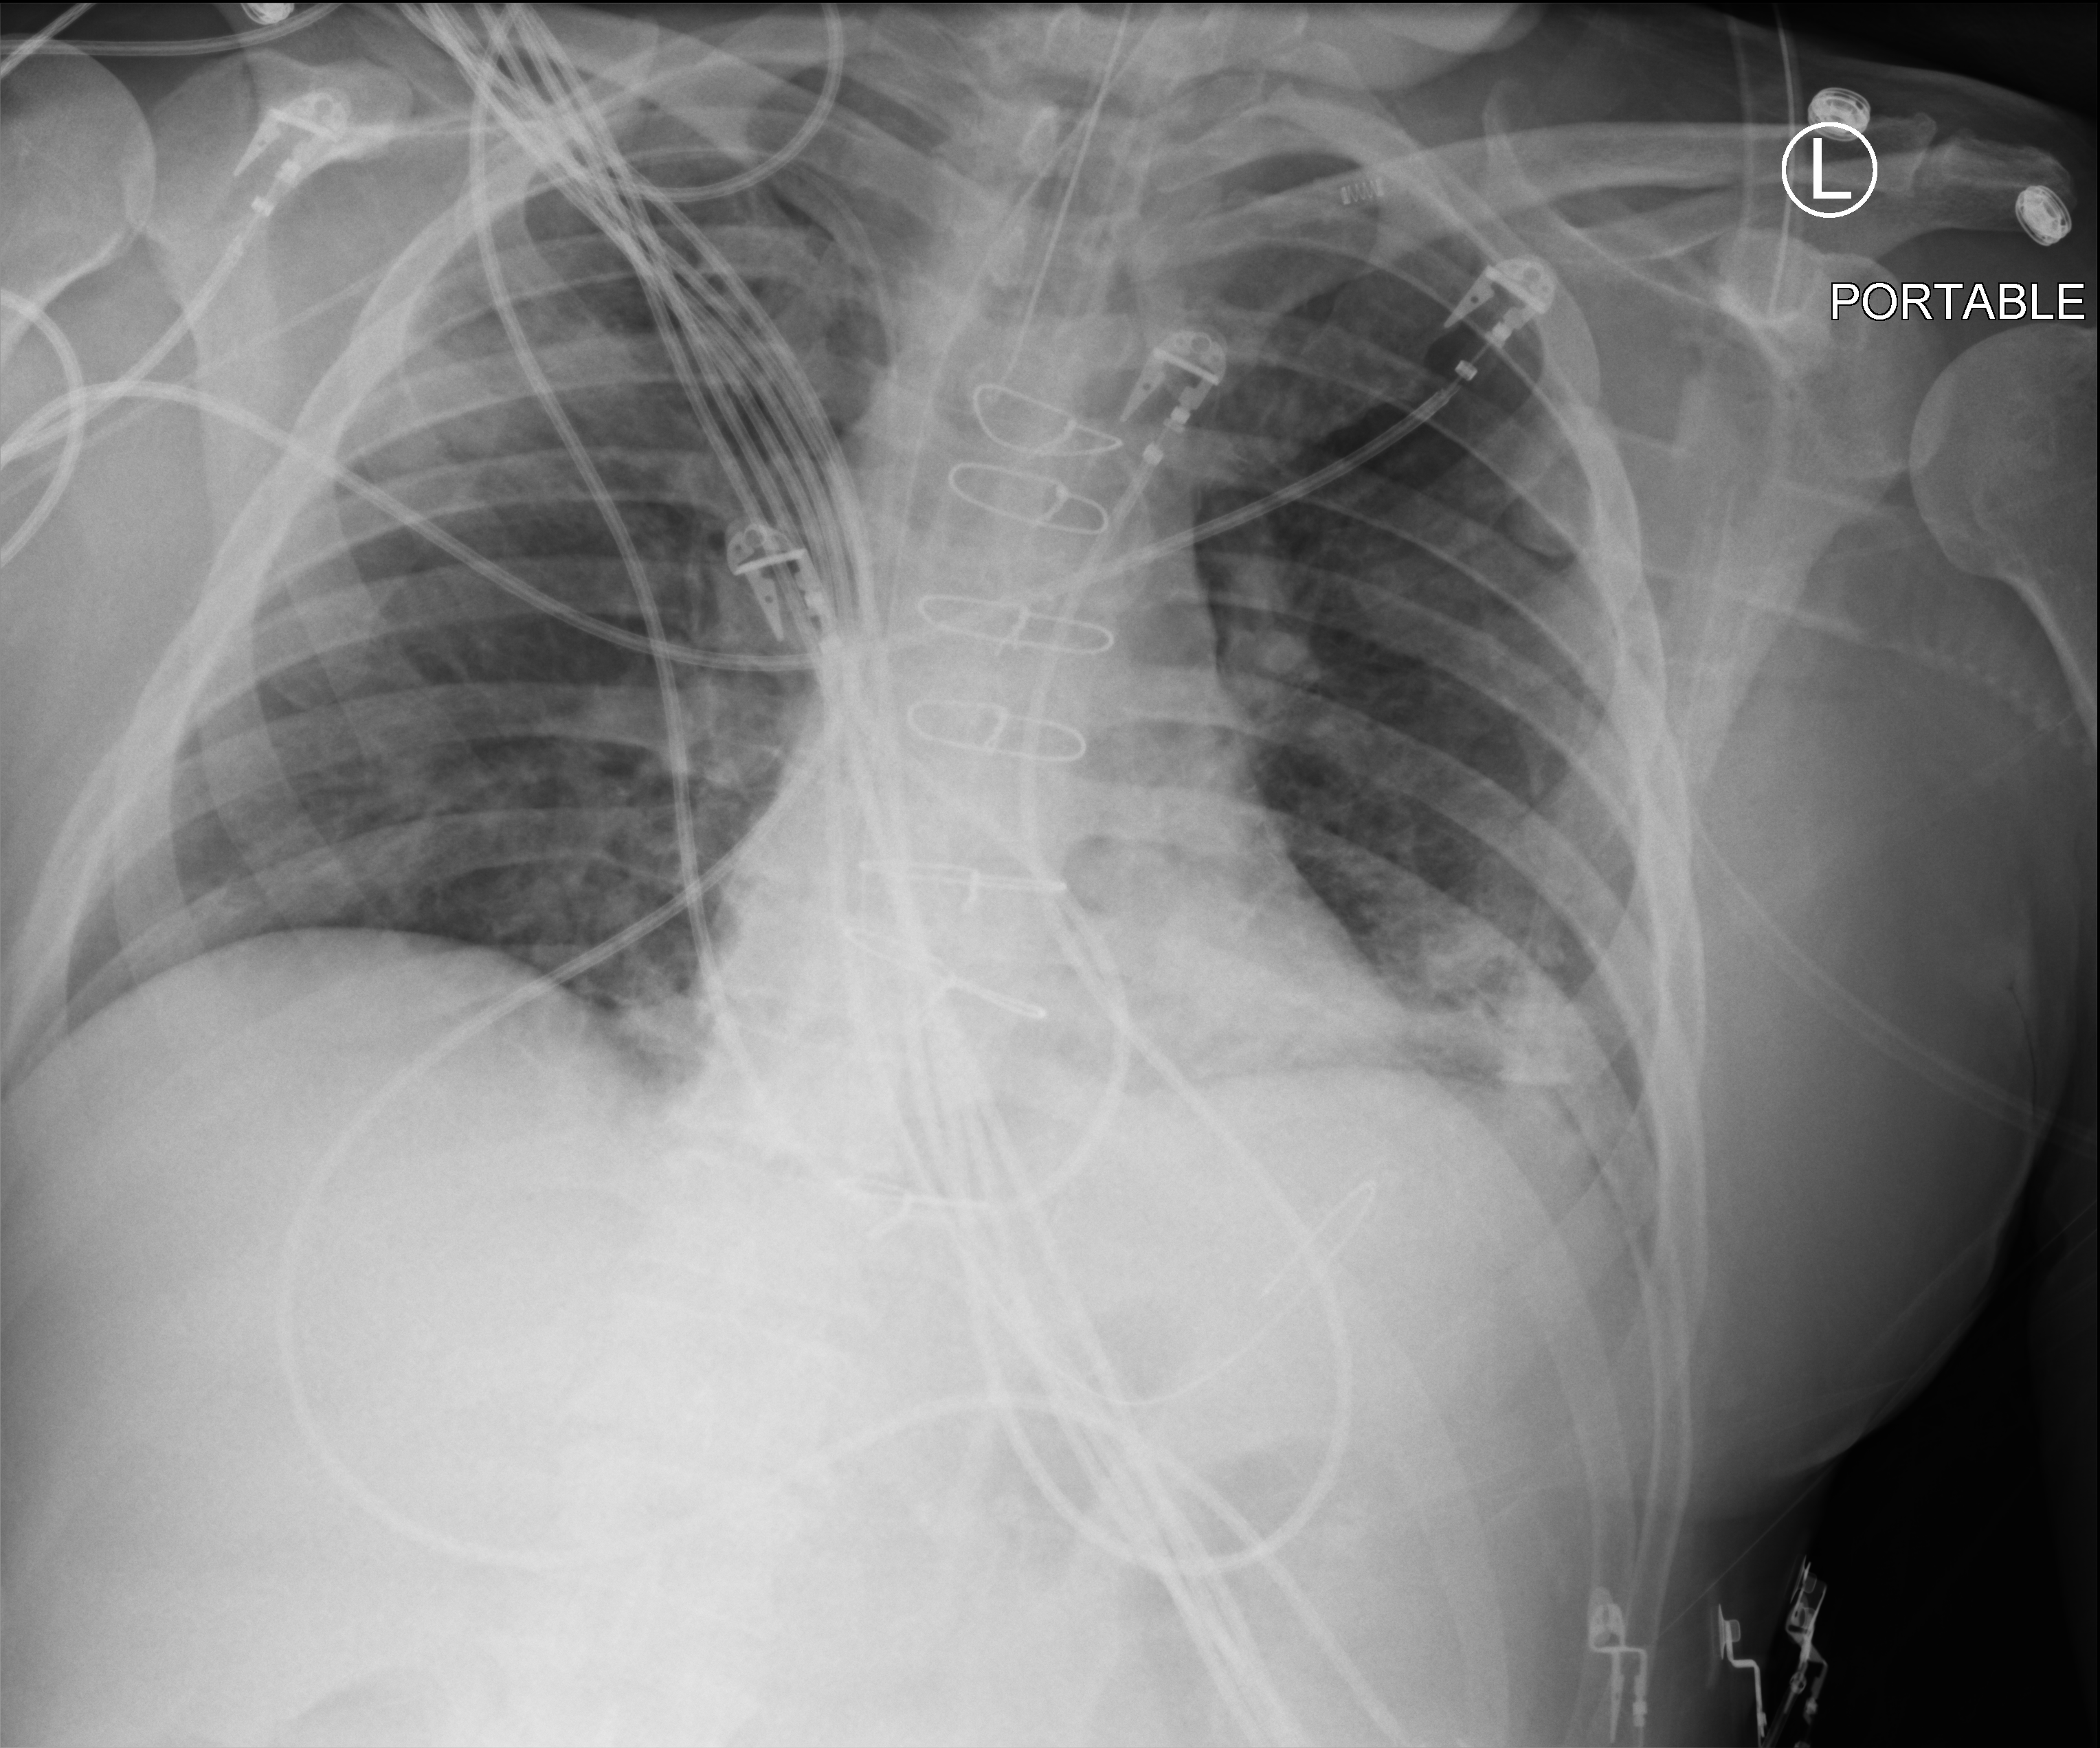
Portable chest radiograph, anteroposterior (AP) projection. Patient hospitalised with COVID-19; male, aged 60–74 years.
Admission-level facts for this patient (not findings on this image; timing relative to this image not recorded): admitted to intensive care during this hospital stay: yes; hypertension (admission record): yes; mechanically ventilated during this hospital stay: yes.